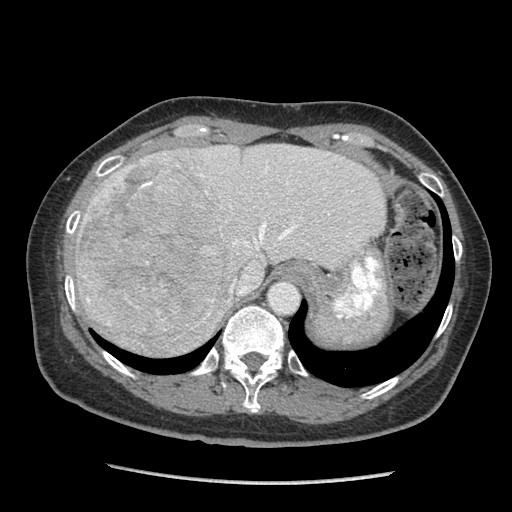
Contrast-enhanced abdominal CT (liver protocol), one axial slice; slice 69 of 105 in the series (ordered by position); reconstruction kernel STANDARD; 140 kVp; soft-tissue window (W 400 / L 40 HU); 2.5 mm slice thickness; 512 × 512 image matrix, field of view 340 × 340 mm. From the clinical record (not read from this slice): diagnosis: hepatocellular carcinoma (patient treated with transarterial chemoembolisation; whether this scan precedes or follows treatment is not stated here); TNM stage (as recorded): Stage-I; Child-Pugh class: A; tumour nodularity: uninodular; tumour size: 11.1 cm.
Outlined on this slice (semi-automatically segmented with operator editing):
- abdominal aorta: bounding box [x1, y1, x2, y2] px = [268, 281, 298, 314]
- liver parenchyma outside the tumour (the mass and vessels are separate outlines, so this box may not span the whole liver): [74, 144, 386, 354]
- mass: [74, 155, 230, 356]
- liver vessels: [200, 166, 297, 292]